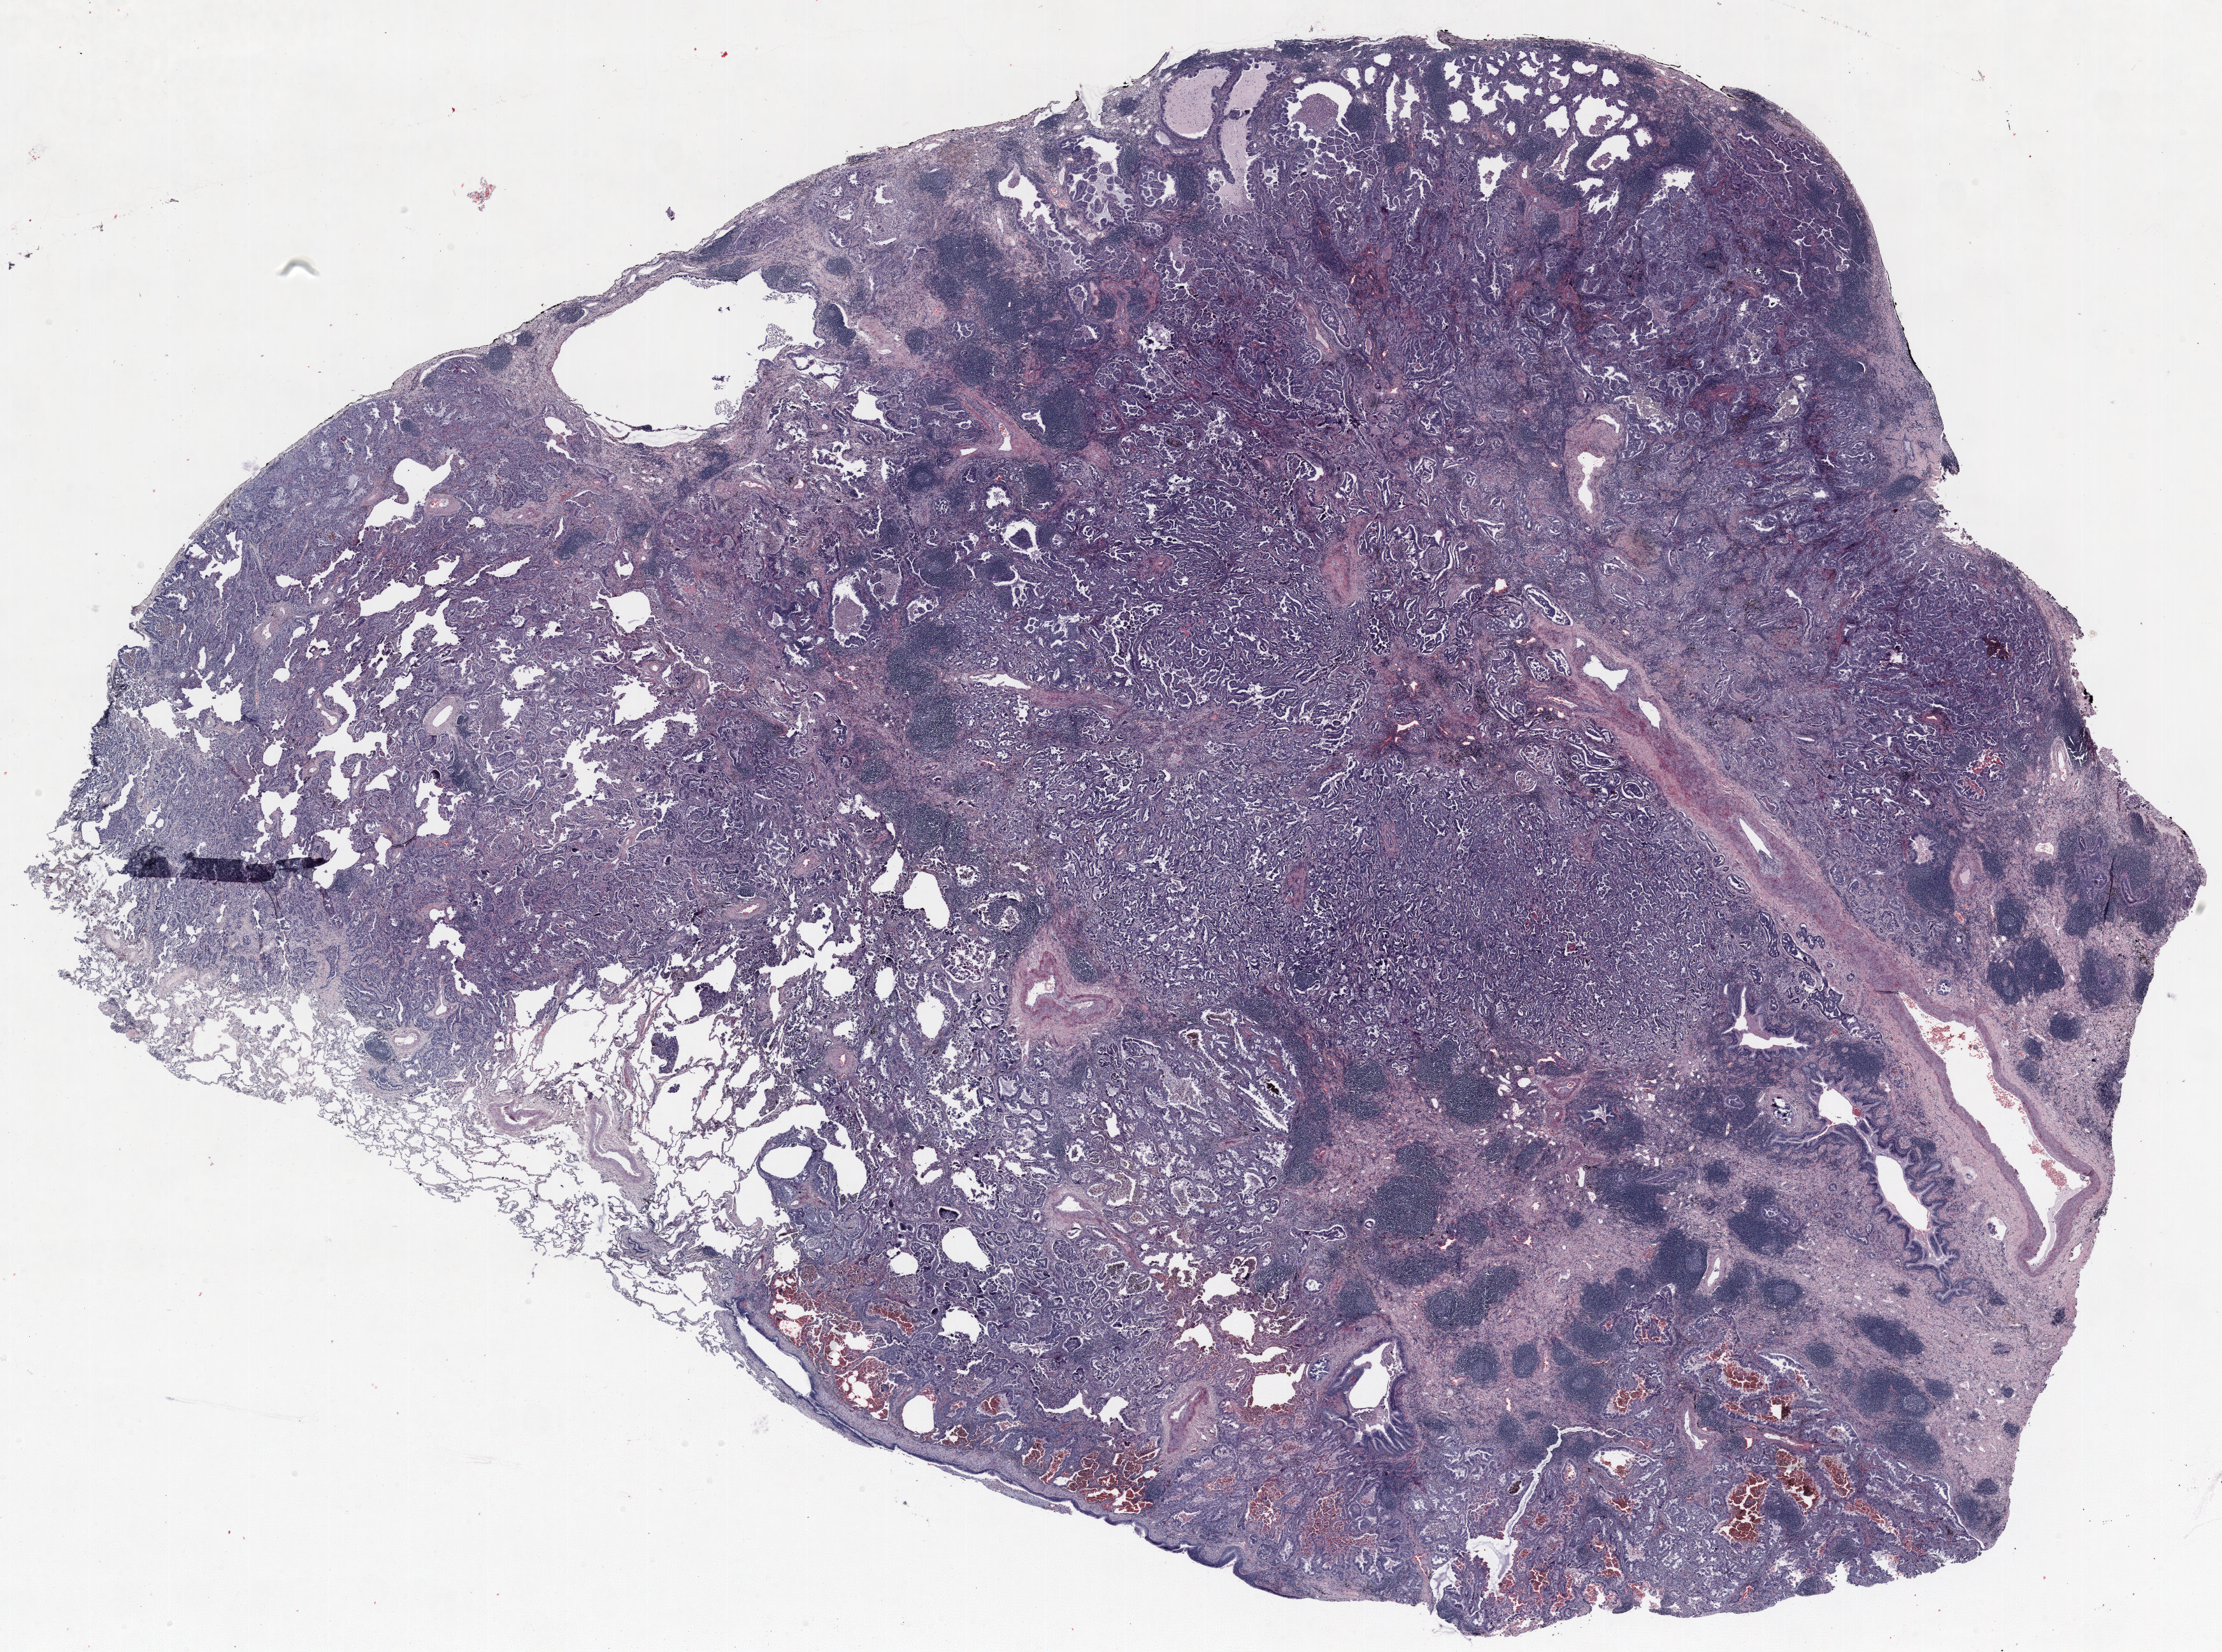
Hematoxylin and eosin (H&E) stained whole-slide image, a low-resolution overview of the entire scanned area, about 28.0 x 20.8 mm (acquisition: 20x scan), formalin-fixed paraffin-embedded (FFPE) section, lung tissue. Female patient, aged 57 at enrolment.
Participant's lung-cancer diagnosis: Adenocarcinoma, NOS (ICD-O-3 8140/3).